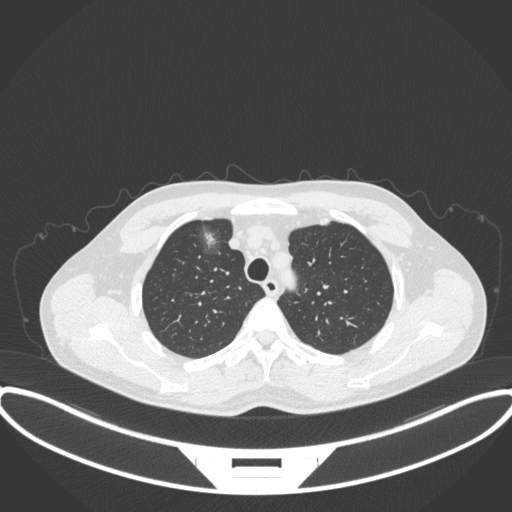
Chest CT, one axial slice. Slice 292 of 395 in the series (ordered by position). 120 kVp. Lung window (W 1500 / L -600 HU). 1 mm slice thickness. 512 × 512 image matrix. Male patient, age 60 years. From the clinical record (not read from this slice): clinical TNM (as recorded): T1c N0 M0.
Structures marked on this image (rectangle marked by the reading radiologist):
- lung tumour (recorded histology: adenocarcinoma): bounding box (x1, y1, x2, y2) in pixels: (195, 217, 227, 261)